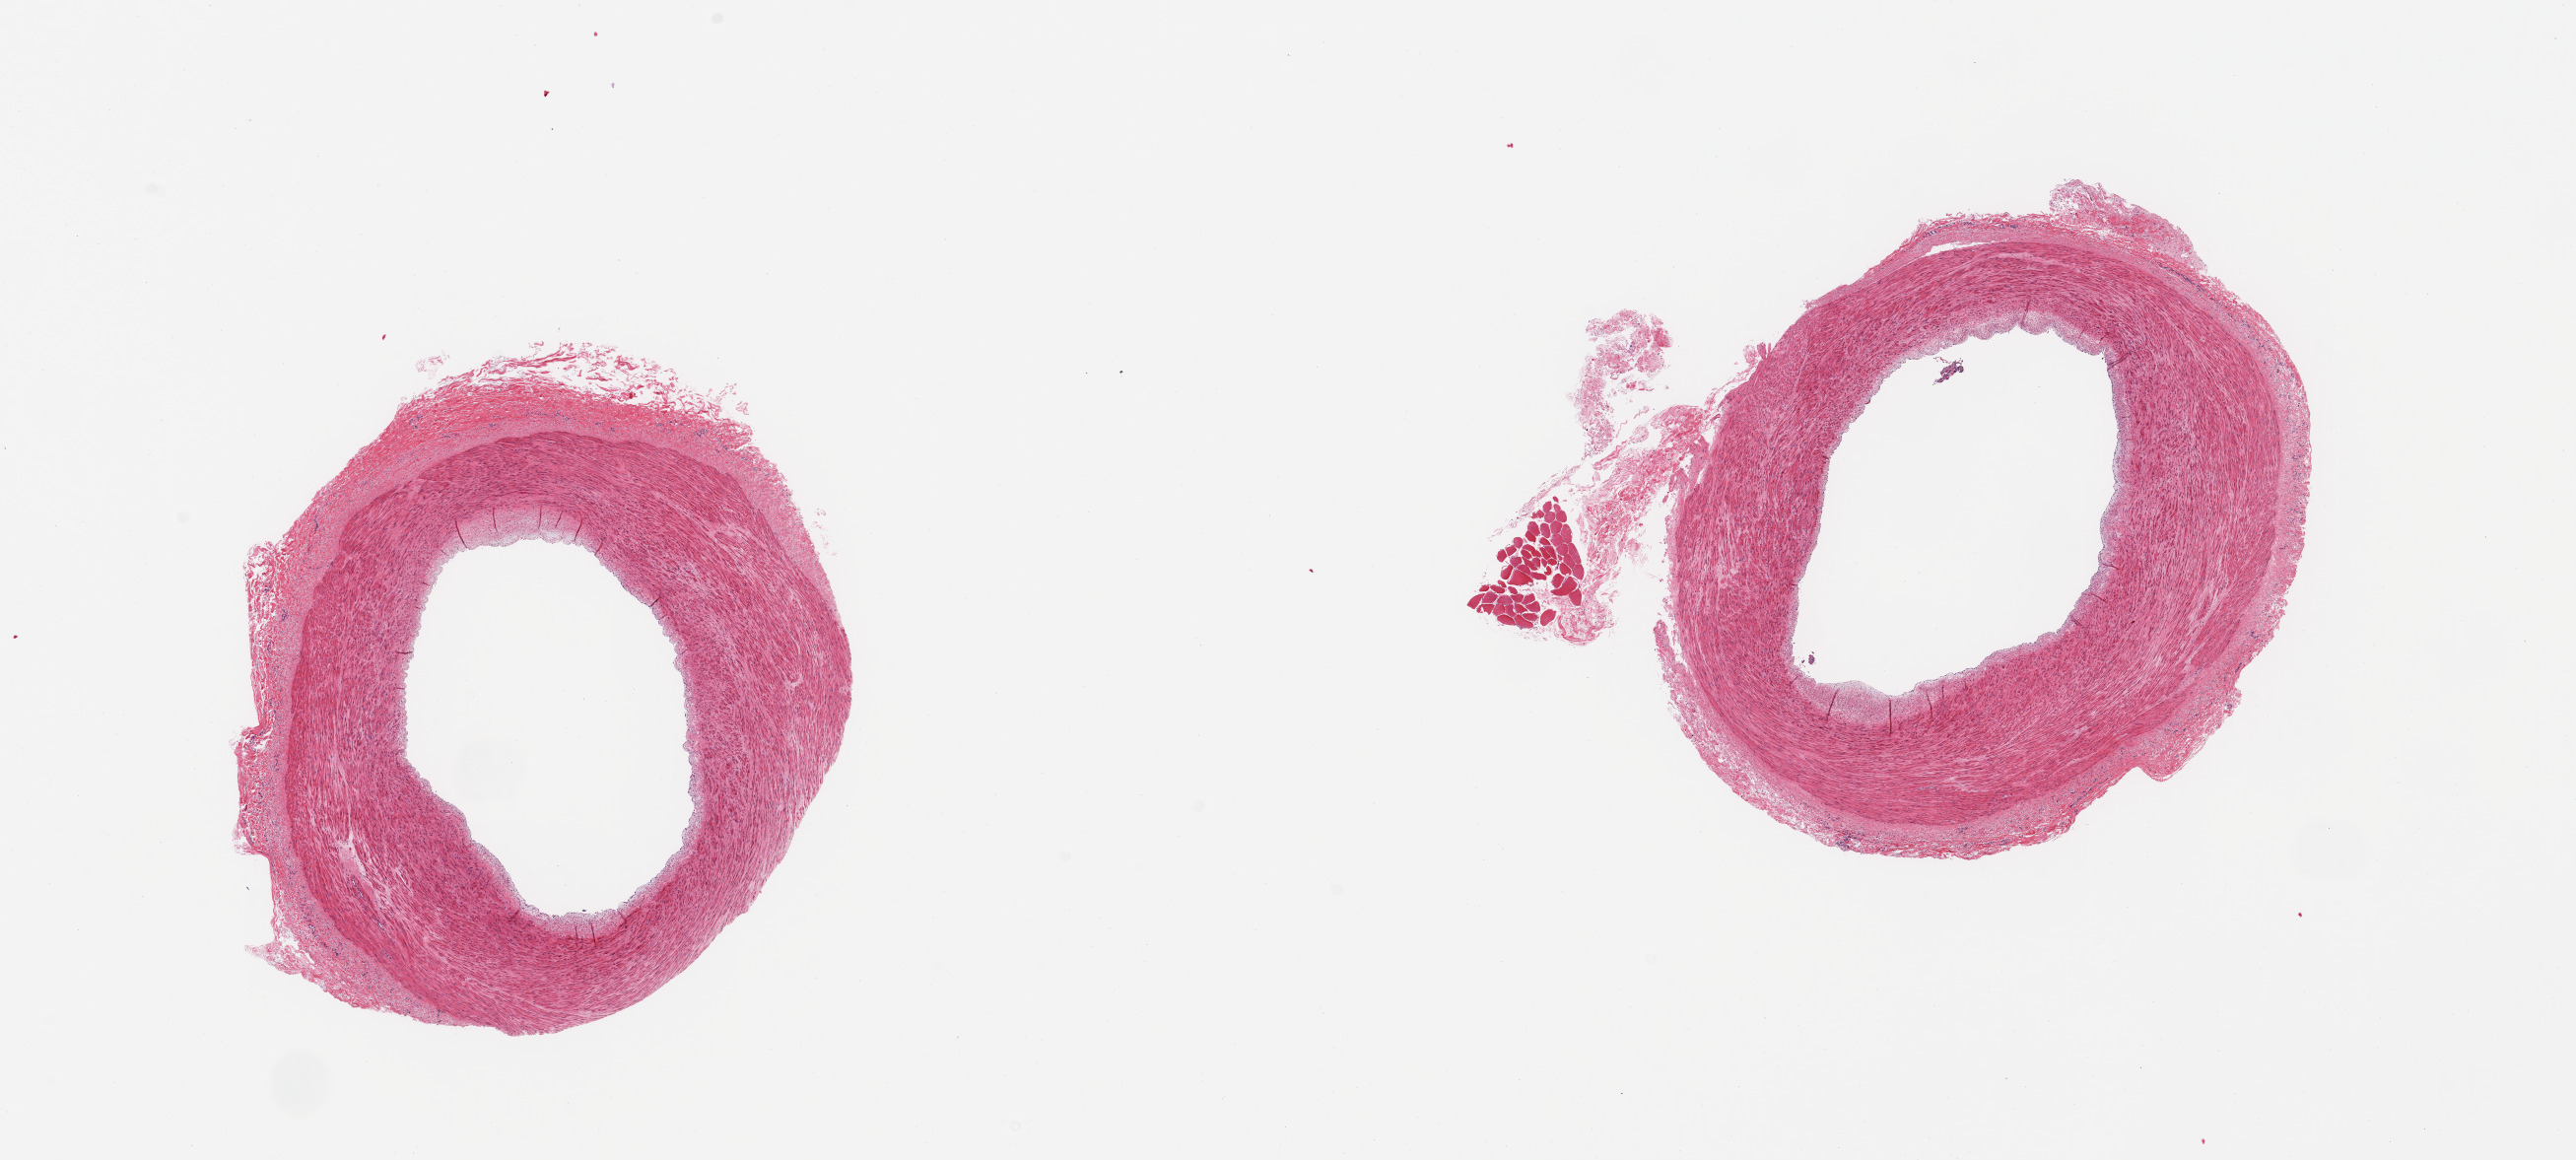
Digitized hematoxylin and eosin (H&E)-stained section, low-resolution overview of the scanned area, about 20.7 x 9.3 mm. PAXgene-fixed, paraffin-embedded tissue. Section of tibial artery (target tissue). Donor tissue sample.
Pathologist's review note for this sample: 2 pieces; up to 0.6mm rim of adventitia and one small fragment of attached skeletal muscle.